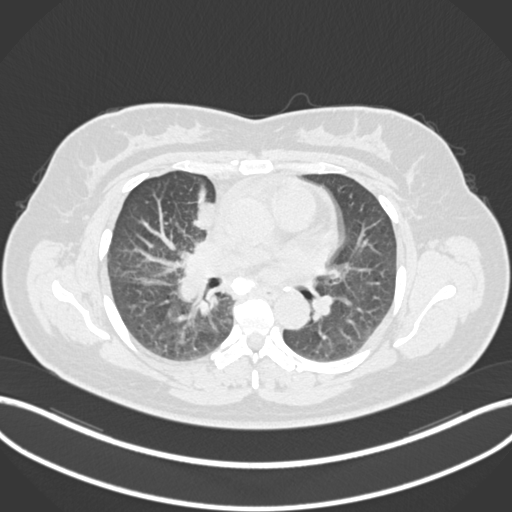
Chest CT, one axial slice; position 91 of 183 along the scan axis; lung window (W 1500 / L -600 HU); 1 mm slice thickness; 512 × 512 image matrix. Female patient, age 46 years. Case-level facts recorded for this patient, not image findings: clinical TNM (as recorded): T2a N1 M0.
Outlined on this slice (rectangle marked by the reading radiologist):
- lung tumour (recorded histology: adenocarcinoma): bounding box (x1, y1, x2, y2) in pixels: (189, 192, 217, 234)